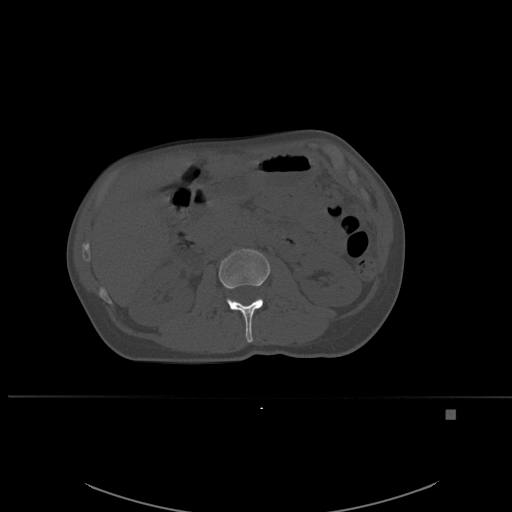
CT including the spine, one axial slice; slice 233 of 537 in the series (ordered by position); bone window (W 1800 / L 400 HU); 1.5 mm slice thickness; 512 × 512 image matrix, field of view 440 × 440 mm. Female patient, age 45 years. From the clinical record (not read from this slice): primary cancer: lung.
Outlined on this slice (semi-automatically segmented with operator editing):
- L2 vertebra: bounding box (x1, y1, x2, y2) in pixels: (219, 249, 270, 343)